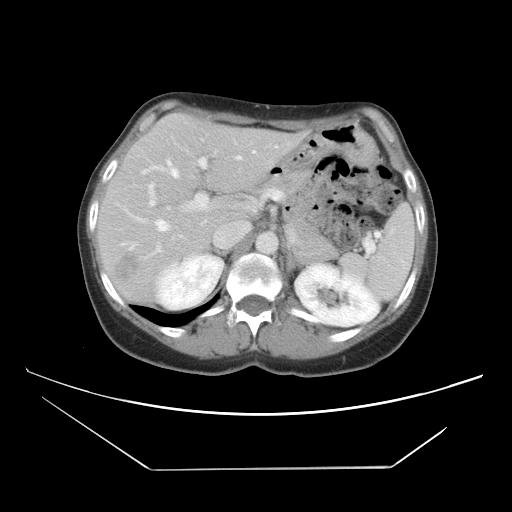
Contrast-enhanced abdominal CT, one axial slice. Slice 28 of 42 in the series (ordered by position). Intravenous contrast given. Soft-tissue window (W 400 / L 40 HU). 5 mm slice thickness. 512 × 512 image matrix. Female patient, age 52 years. Case-level facts recorded for this patient, not image findings: diagnosis: colorectal cancer liver metastases, imaged before liver resection; multiple liver metastases: yes; largest metastasis: 5.5 cm.
Outlined on this slice (manually delineated by an expert):
- hepatic veins: bounding box [x1, y1, x2, y2] px = [124, 146, 277, 244]
- liver: [100, 116, 299, 304]
- planned liver remnant (the part of the liver to remain after resection): [115, 117, 228, 225]
- portal vein (with intrahepatic branches): [148, 149, 284, 212]